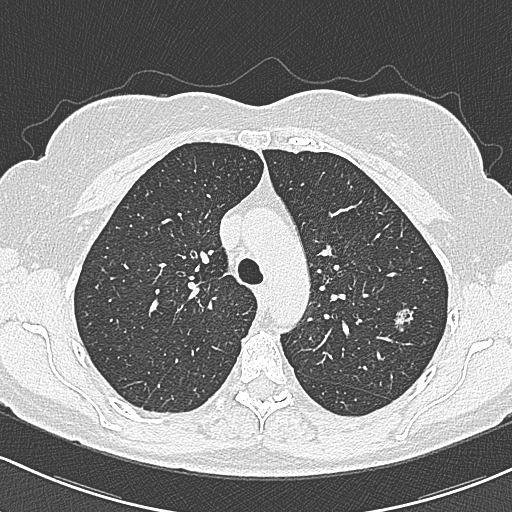
Axial slice from a low-dose chest CT screening exam, first (baseline) screen, lung window (W 1500 / L -600 HU). Female participant, aged 65 years at enrolment. Current smoker at enrolment.
- Lesion marked by an expert reader, bounding box [x1, y1, x2, y2] px = [381, 298, 423, 337].
- The screening reader recorded 3 non-calcified nodules or masses ≥4 mm on this exam; which of them this box marks is not recorded.
- Lung cancer was diagnosed 390 days after this screen: bronchiolo-alveolar carcinoma, non-mucinous, left upper lobe, stage IA (AJCC 6th edition), 10 mm at pathology.